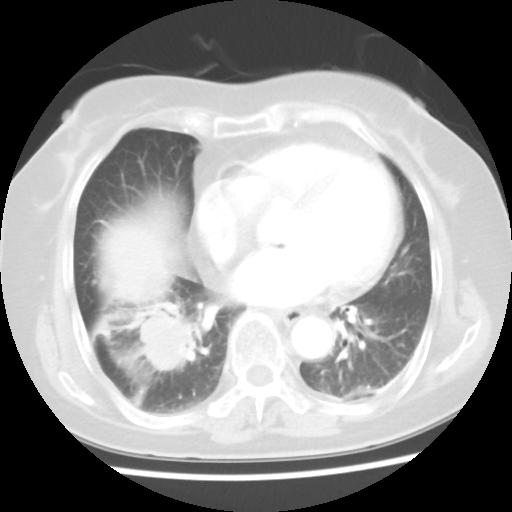
Chest CT, one axial slice; position 17 of 45 along the scan axis; reconstruction kernel STANDARD; lung window (W 1500 / L -600 HU); 5 mm slice thickness; 512 × 512 image matrix, field of view 312 × 312 mm. Patient: female, 65 years. From the clinical record (not read from this slice): clinical TNM (as recorded): T2 N3 M0.
Structures marked on this image (rectangle marked by the reading radiologist):
- lung tumour (recorded histology: adenocarcinoma): bounding box <127,300,210,384> (left, top, right, bottom; pixels)